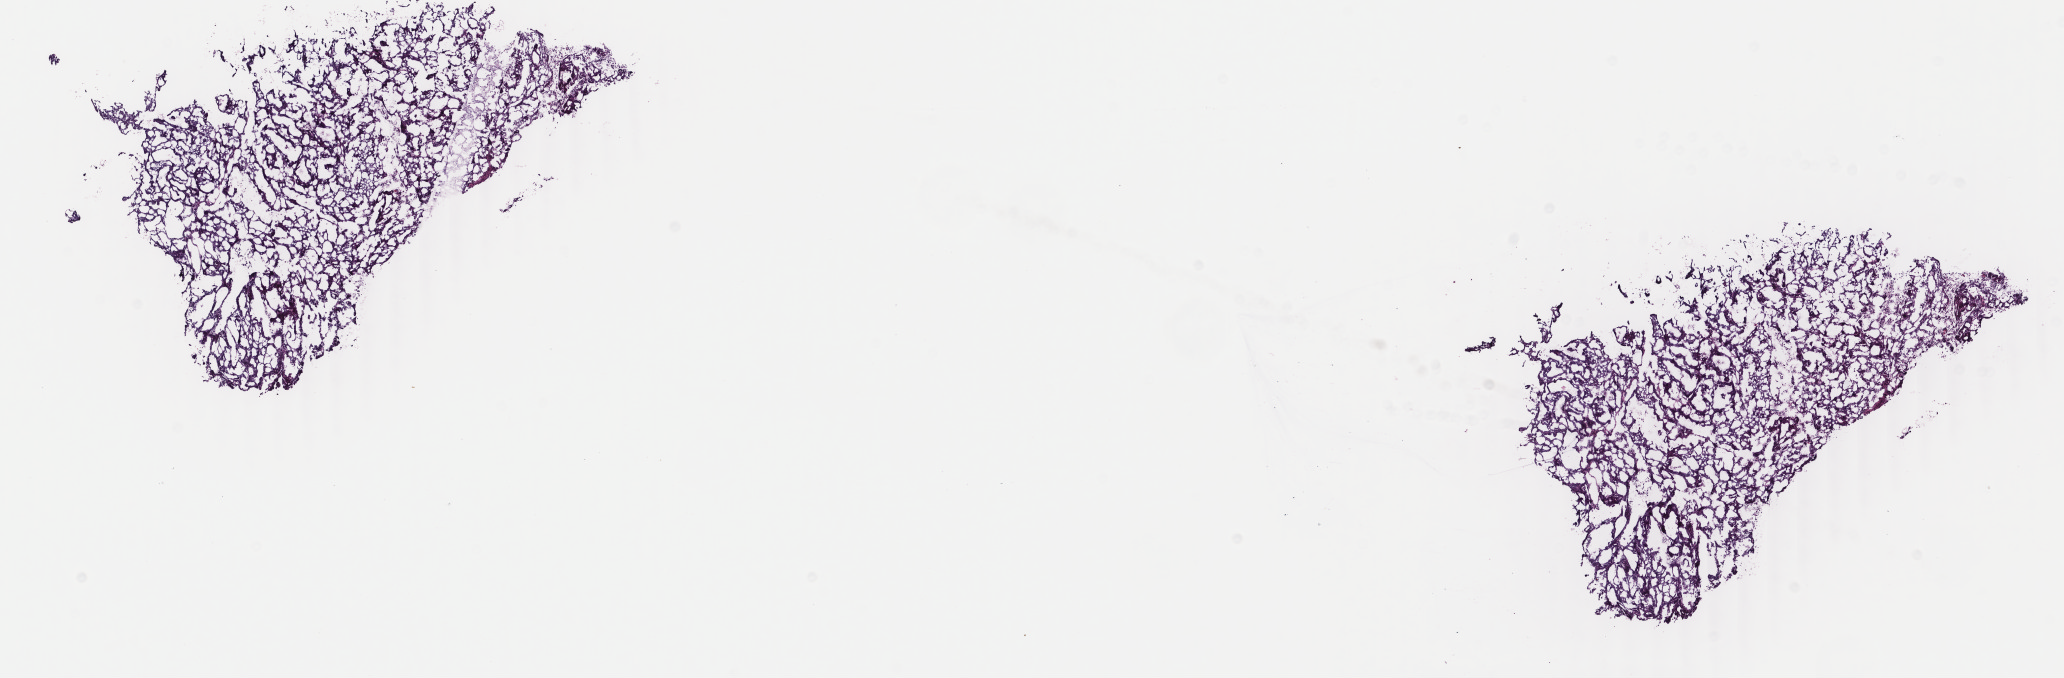
Whole-slide histology image, Hematoxylin and eosin (H&E) stained — shown as a low-resolution overview of the whole scanned area (about 16.4 x 5.4 mm), frozen section from the bottom of the tissue portion, primary tumour sample from the uterus. Patient: female, age at initial diagnosis 60 years. Histologic grade: G2 (moderately differentiated). Slide review estimates, as recorded: tumour cells 100%, tumour nuclei 80%, normal cells 0%, stromal cells 0%, necrosis 0%. Infiltration values recorded for this section: lymphocyte infiltration 0%, monocyte infiltration 0%, neutrophil infiltration 0%.
FIGO stage: IB. Diagnosis: Endometrioid adenocarcinoma, NOS (endometrium).